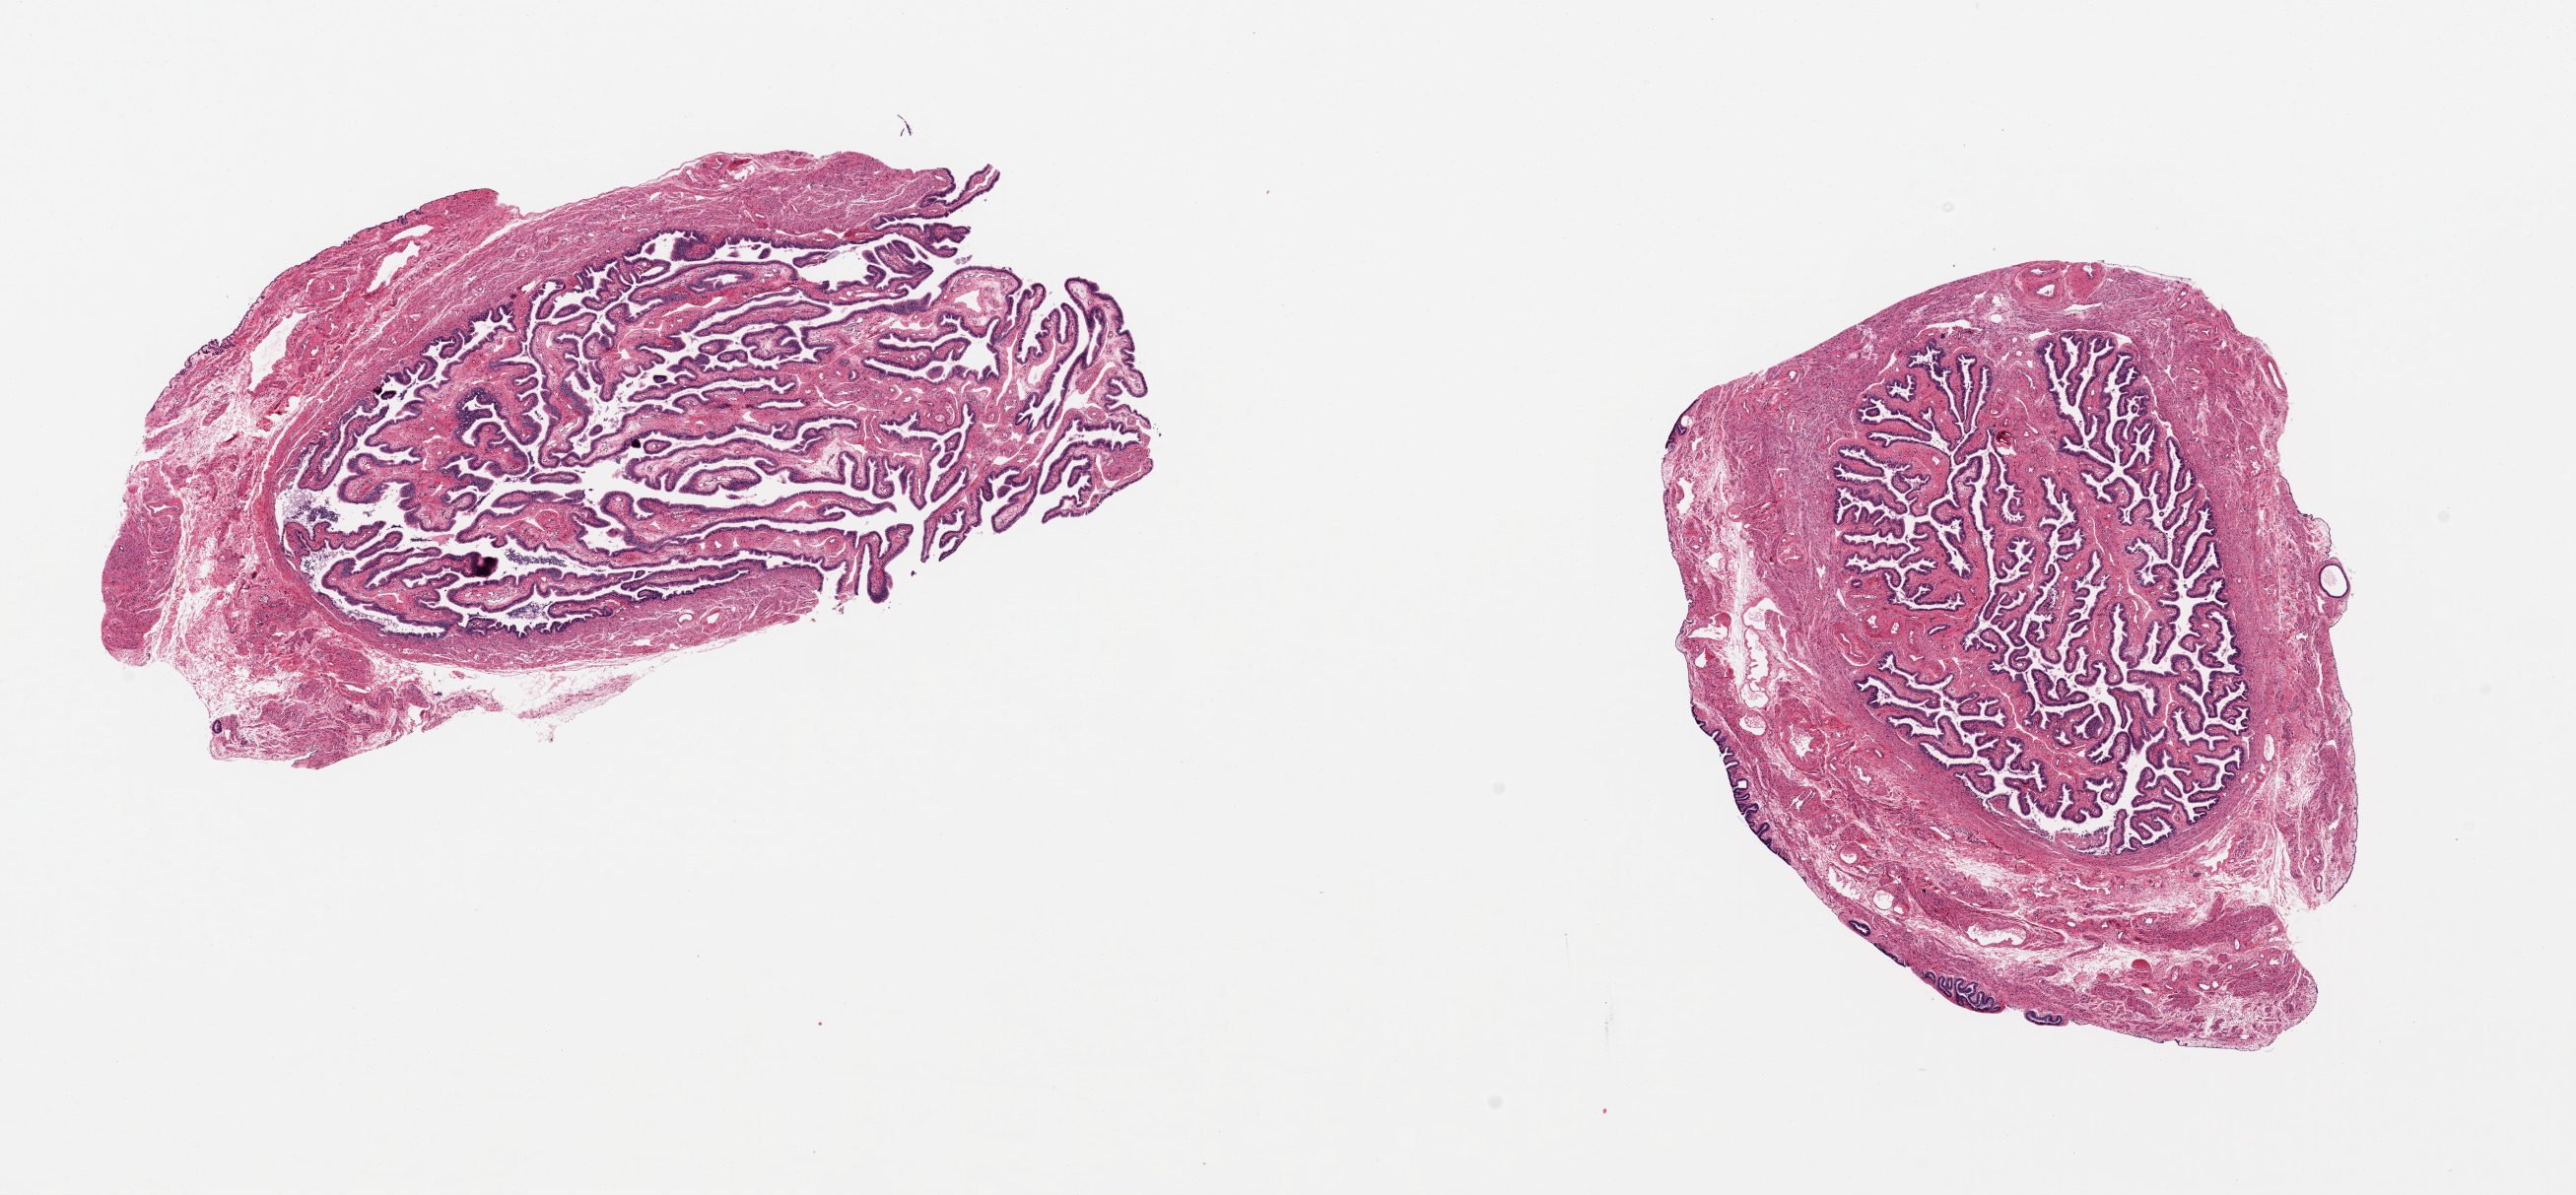
Hematoxylin and eosin (H&E) whole-slide image, shown as a low-resolution overview of the whole scanned area (about 20.7 x 9.6 mm); PAXgene-fixed paraffin-embedded (PFPE) section; target tissue: fallopian tube; donor tissue sample. Donor: female.
- pathologist's review note for this sample: 2 pieces 8x3 & 6x5 mm; excellent preservation